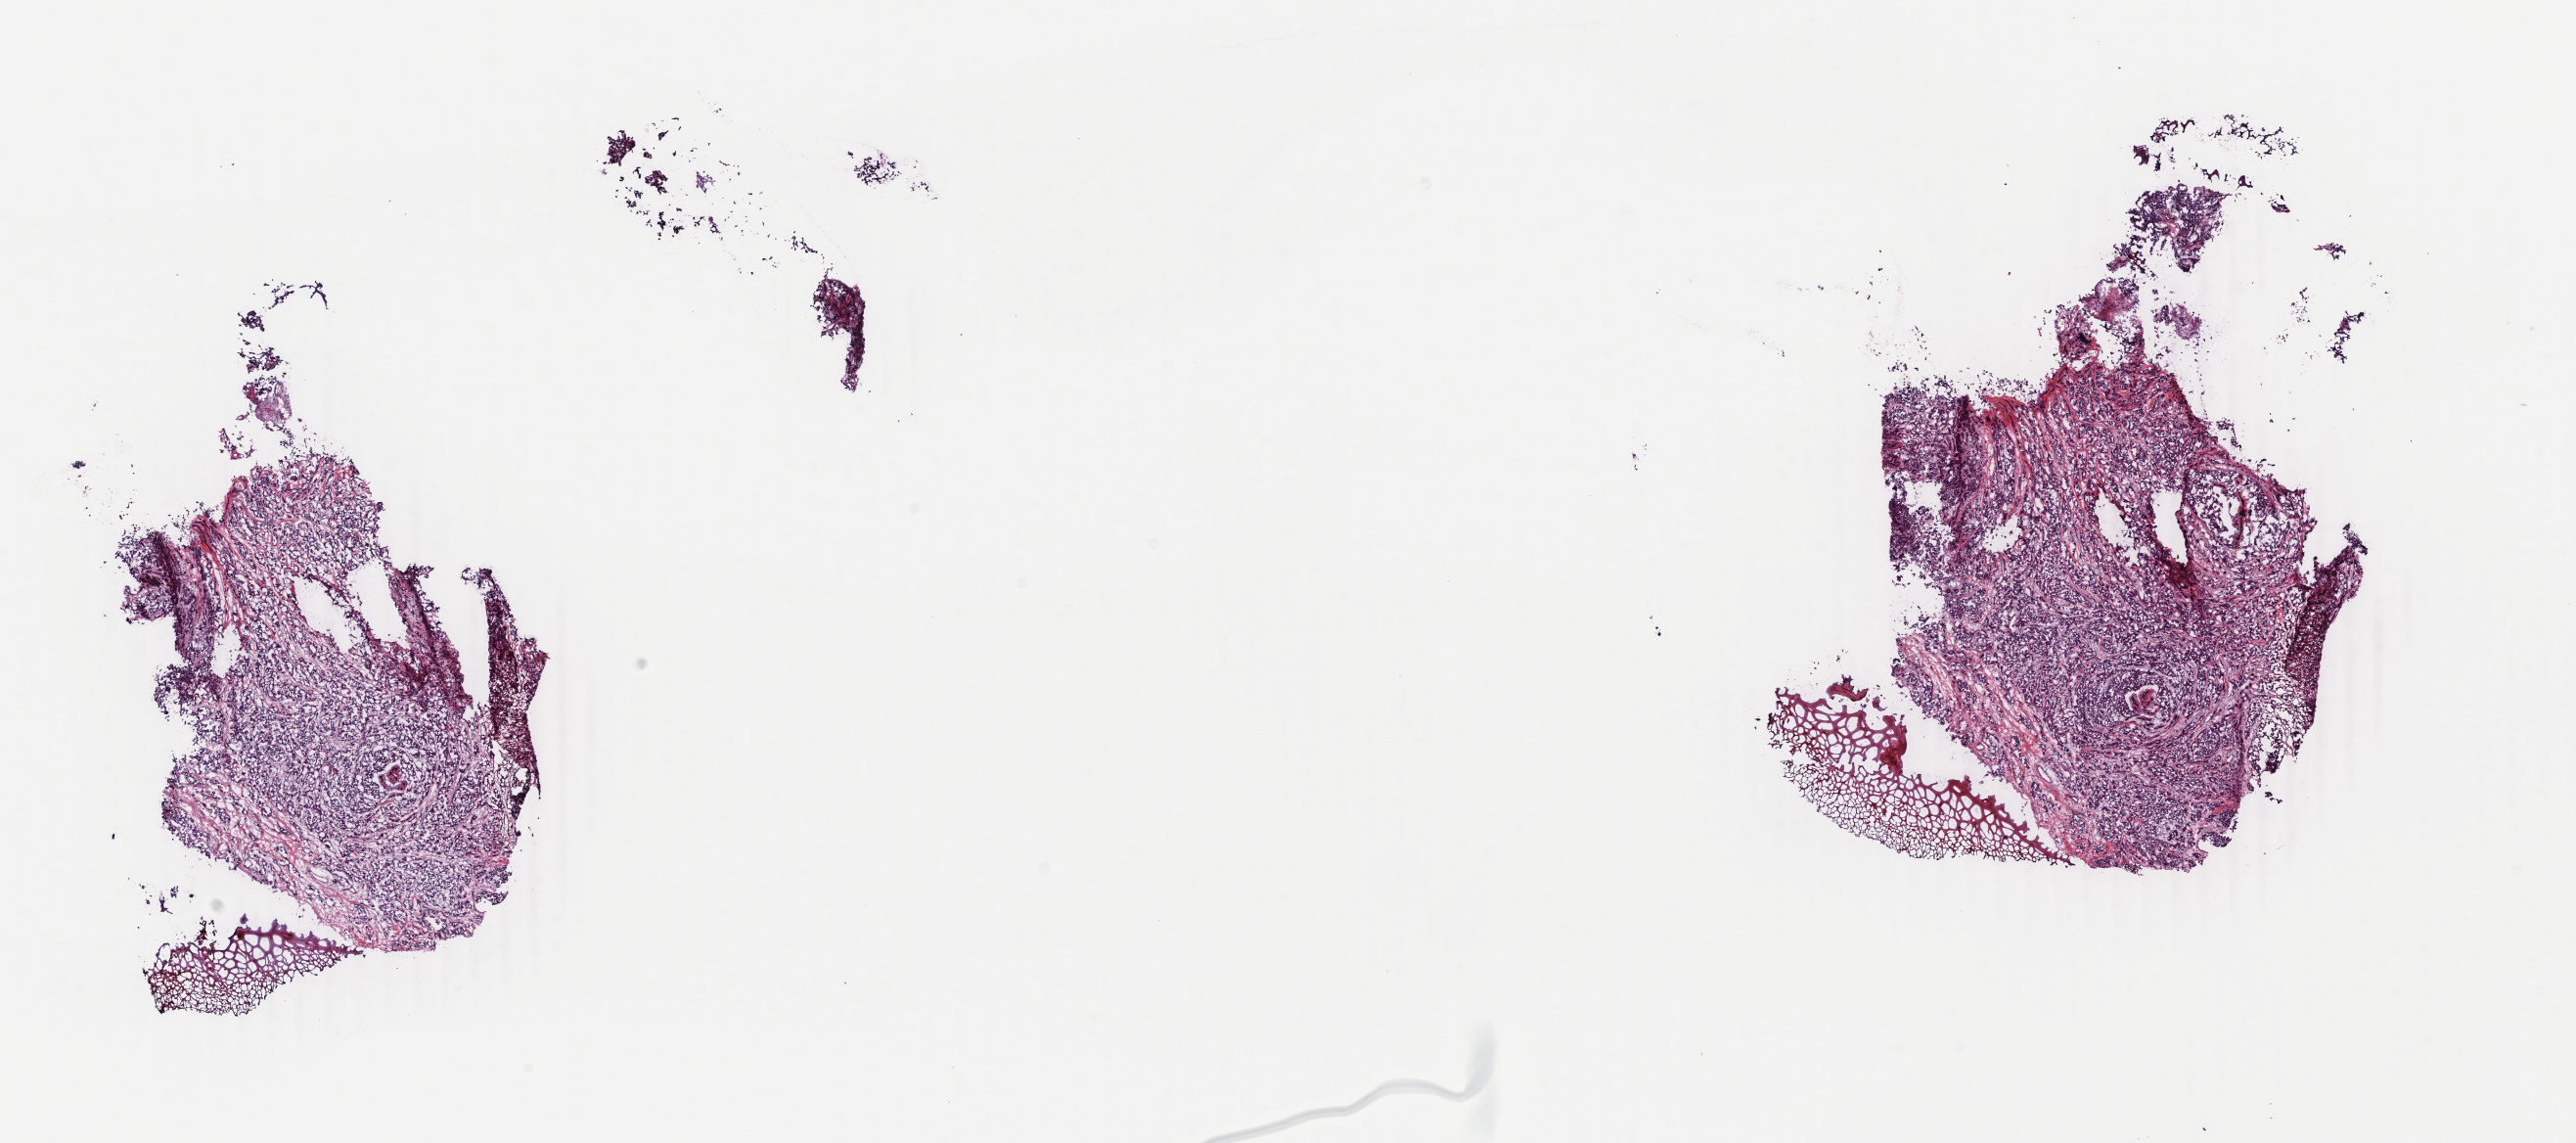
Hematoxylin and eosin (H&E) stained whole-slide image, low-resolution overview of the scanned area, about 20.9 x 9.3 mm; frozen section from the bottom of the tissue portion; breast, primary tumour sample. Patient: female, age at initial diagnosis 26 years. Slide review estimates, as recorded: tumour cells 80%, tumour nuclei 90%, normal cells 0%, stromal cells 20%, necrosis 0%. Inflammatory infiltration, as recorded: lymphocyte infiltration 0%, monocyte infiltration 0%, neutrophil infiltration 0%.
Pathologic diagnosis: Infiltrating duct carcinoma, NOS. AJCC pathologic stage: IIB (4th edition). Lymph nodes positive (case pathology): 0 of 19 examined.